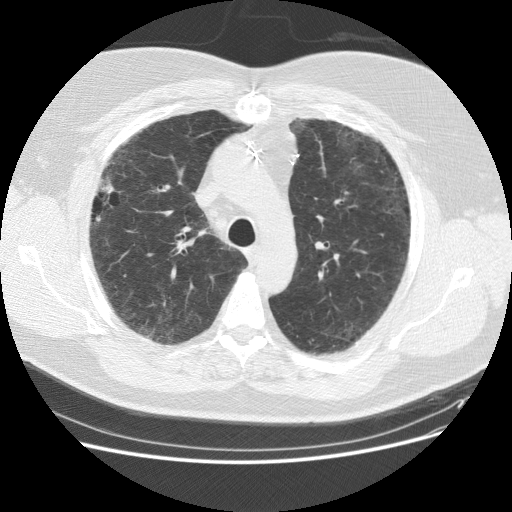
Chest CT (low-dose screening protocol), one axial image; baseline screening round; lung window (W 1500 / L -600 HU); standard (soft-tissue) reconstruction kernel (STANDARD); 512 × 512 image matrix, field of view 378 × 378 mm. Male, age 59 years at enrolment.
• Expert reader's lesion annotation, box from (x=74, y=158) to (x=138, y=245) px.
• The screening reader recorded 2 non-calcified nodules or masses ≥4 mm on this exam (right middle lobe, right lower lobe); which of them this box marks is not recorded.
• Later outcome: lung cancer diagnosed 338 days after this screen — adenocarcinoma, NOS, right upper lobe, right middle lobe, moderately differentiated (G2), stage IA (AJCC 6th edition), 13 mm at pathology.